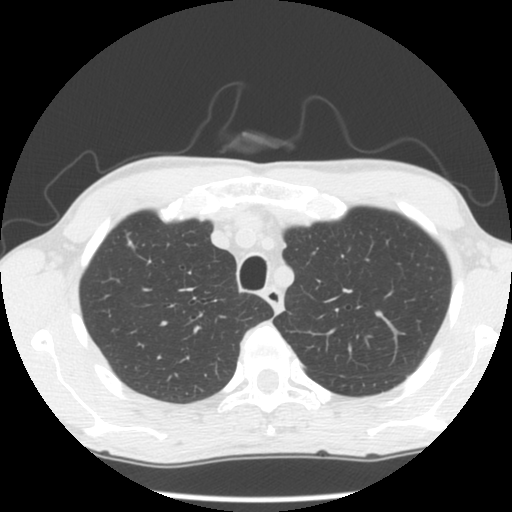
Chest CT (low-dose screening protocol), one axial image, second annual screen, lung window (W 1500 / L -600 HU), standard (soft-tissue) reconstruction kernel (STANDARD). Male, age 56 years at enrolment. Current smoker at enrolment.
Expert-annotated lung lesion, bounding box <107,226,152,269> (left, top, right, bottom; pixels). Screening reader's record for this exam: no non-calcified nodule ≥4 mm recorded. Lung cancer was diagnosed 345 days after this screen: small cell carcinoma, NOS, right upper lobe, stage IV (AJCC 6th edition).